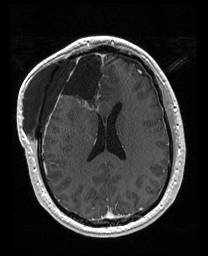
Brain MRI from a brain-tumour surgery series, one axial slice. Slice 76 of 176 in the series (ordered by position). T1-weighted post-contrast. 1 mm slice thickness. 208 × 256 image matrix, field of view 208 × 256 mm. From the clinical record (not read from this slice): histopathology: Astrocytoma; WHO grade: 4; IDH mutation: yes; tumour location: Right Orbitofrontal Anterior Temporal Insular.
Annotated regions visible in this slice (expert manual segmentation):
- previous resection cavity: bounding box (x1, y1, x2, y2) in pixels: (56, 52, 106, 111)